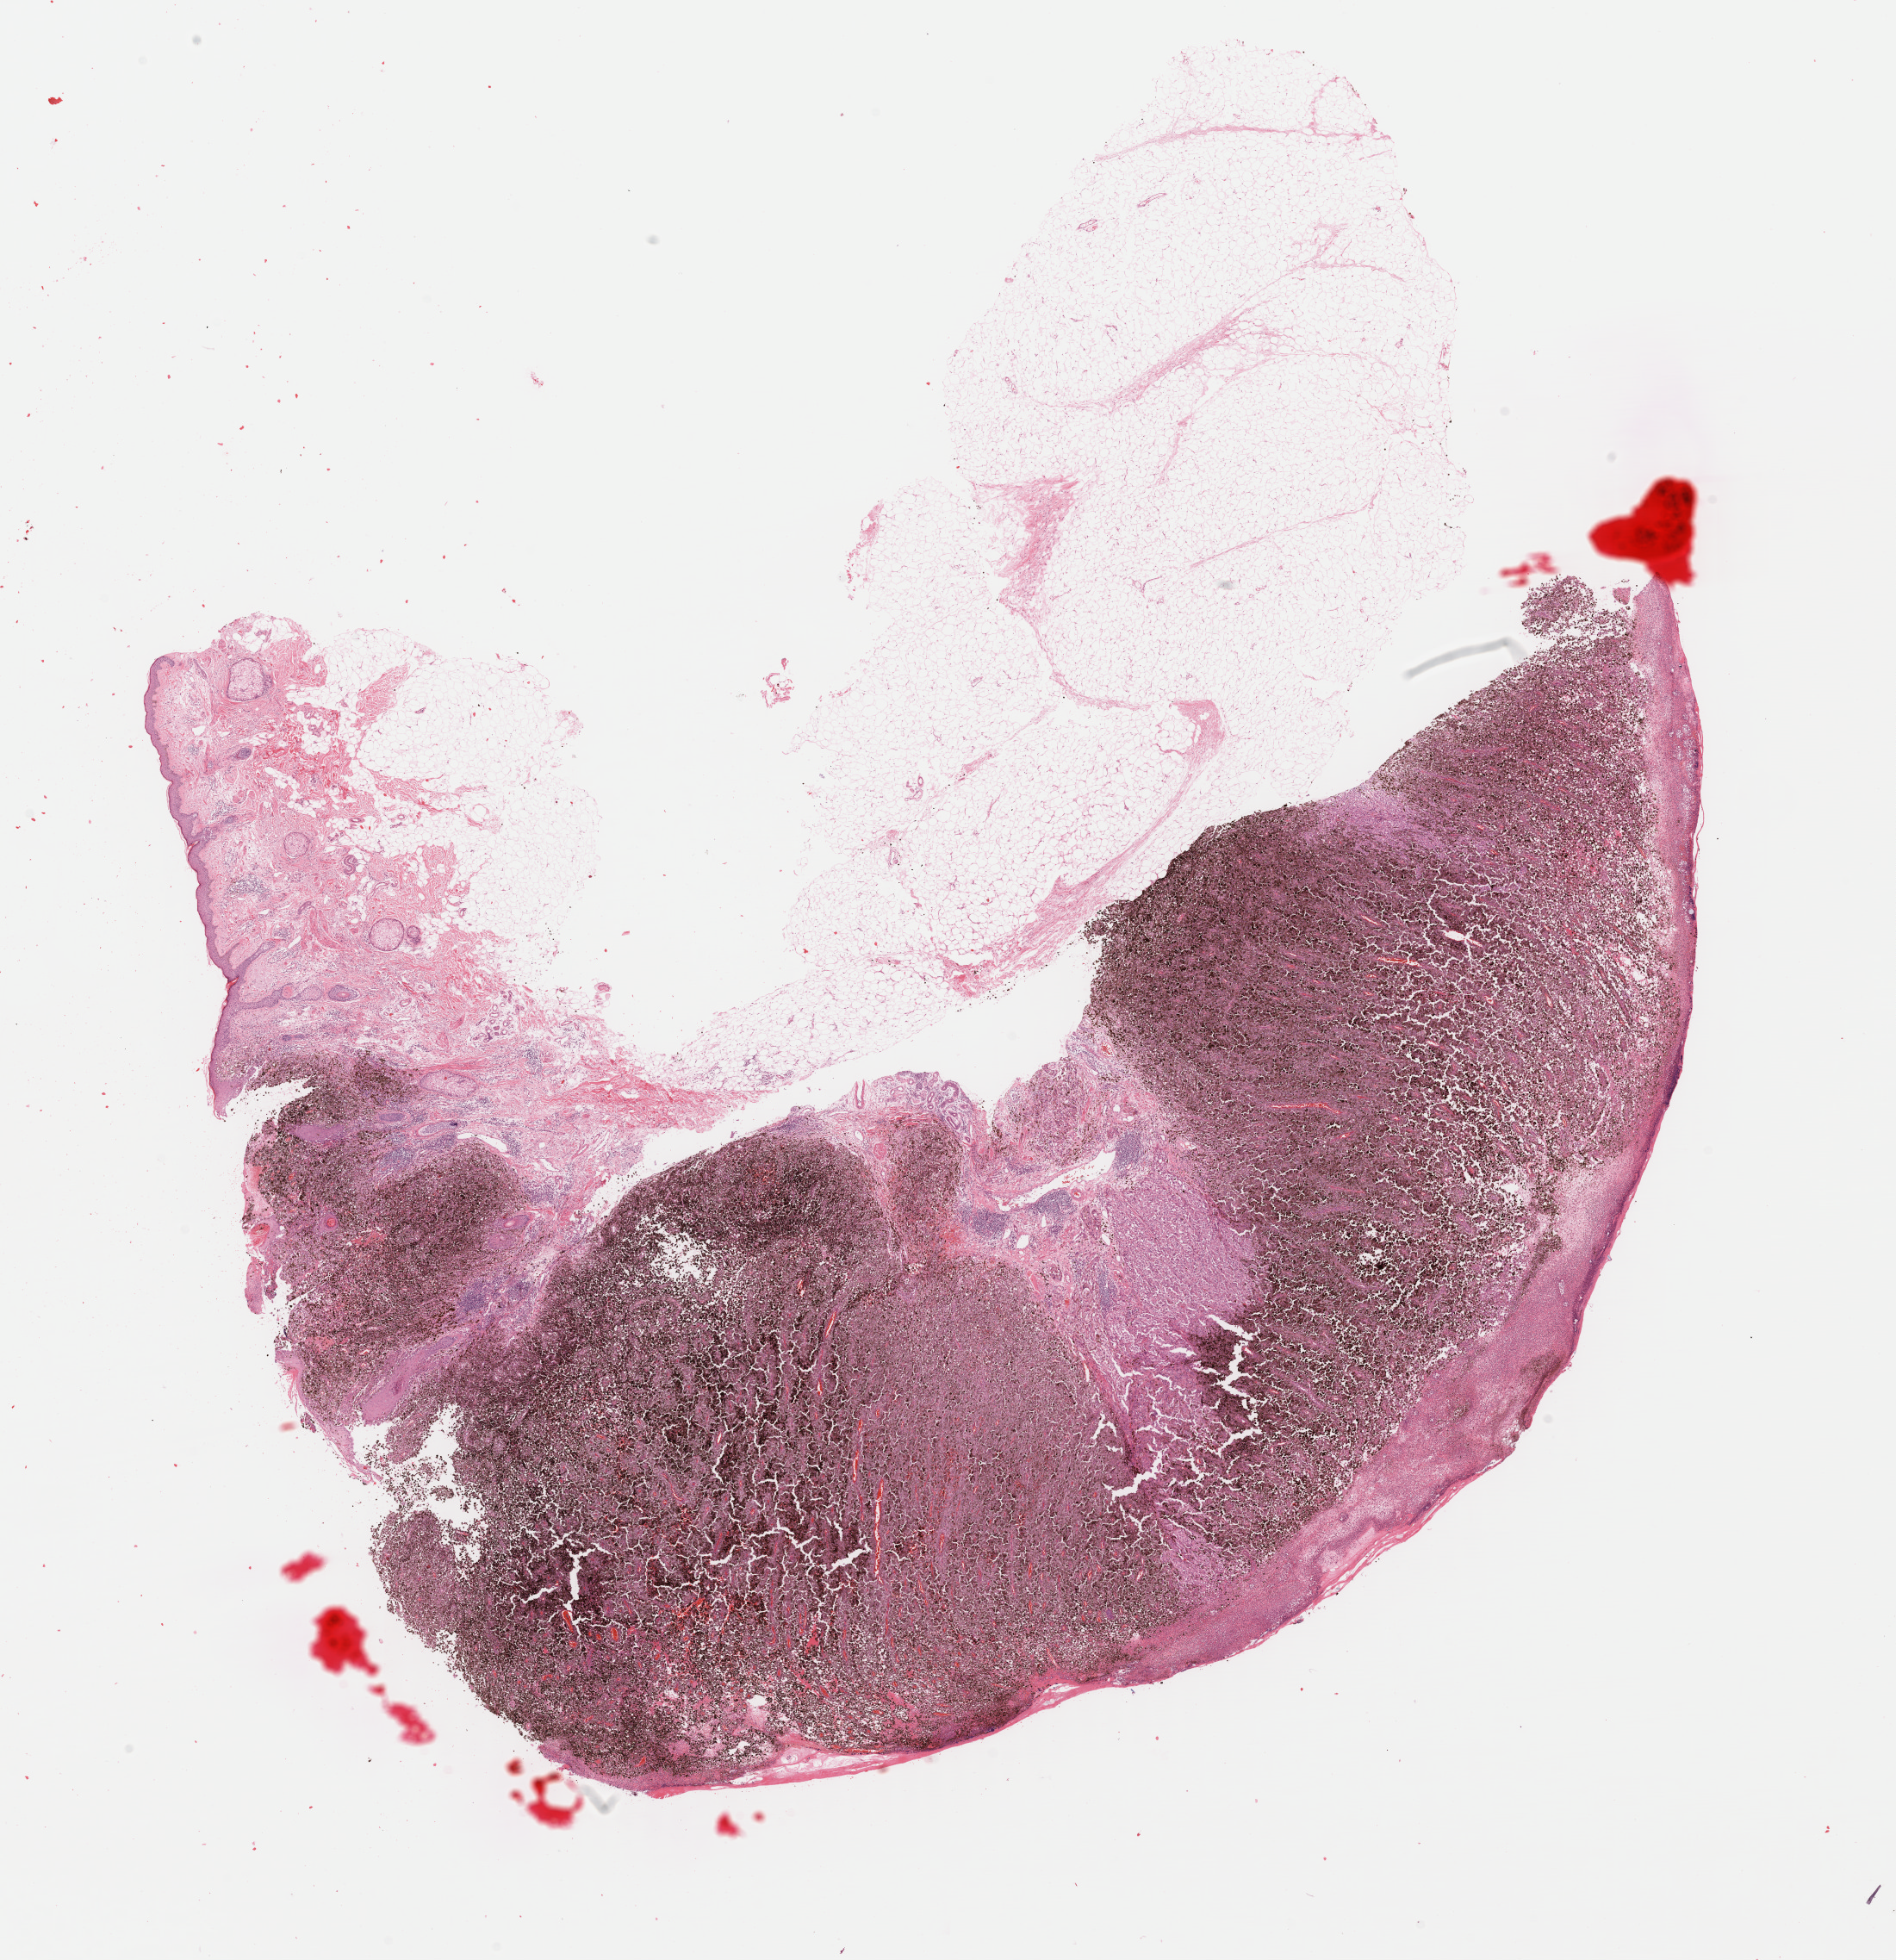
H&E-stained whole-slide image — whole scanned area (about 17.4 x 17.9 mm, from a 40x scan) shown as a low-resolution overview; formalin-fixed paraffin-embedded (FFPE) diagnostic section; skin, primary tumour sample. Patient: female, age at initial diagnosis 86 years.
* diagnosis: Malignant melanoma, NOS
* AJCC pathologic stage: IIIB